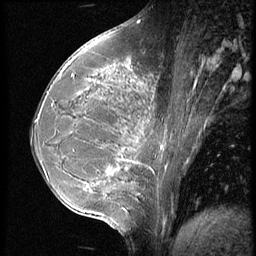
Breast MRI (dynamic contrast-enhanced), one sagittal slice; position 25 of 56 along the scan axis; 3 images stored at this slice position (order not interpretable as contrast timing); 1.5 T; TE 4.2 ms, TR 9 ms; 2.5 mm slice thickness; 256 × 256 image matrix, field of view 180 × 180 mm. Female patient, age 35 years. Case-level facts recorded for this patient, not image findings: setting: breast cancer imaged before/during neoadjuvant chemotherapy; receptor status: HR-positive, HER2-negative.
Outlined on this slice (semi-automatic segmentation, software-assisted and operator-edited):
- analysis volume of interest (the breast-tissue region the enhancement analysis was run in; not a lesion): box from (x=63, y=60) to (x=179, y=218) px
- tumour enhancement mask (voxels above the 140 % enhancement threshold inside the analysis volume of interest): (x=93, y=69)–(x=162, y=186)